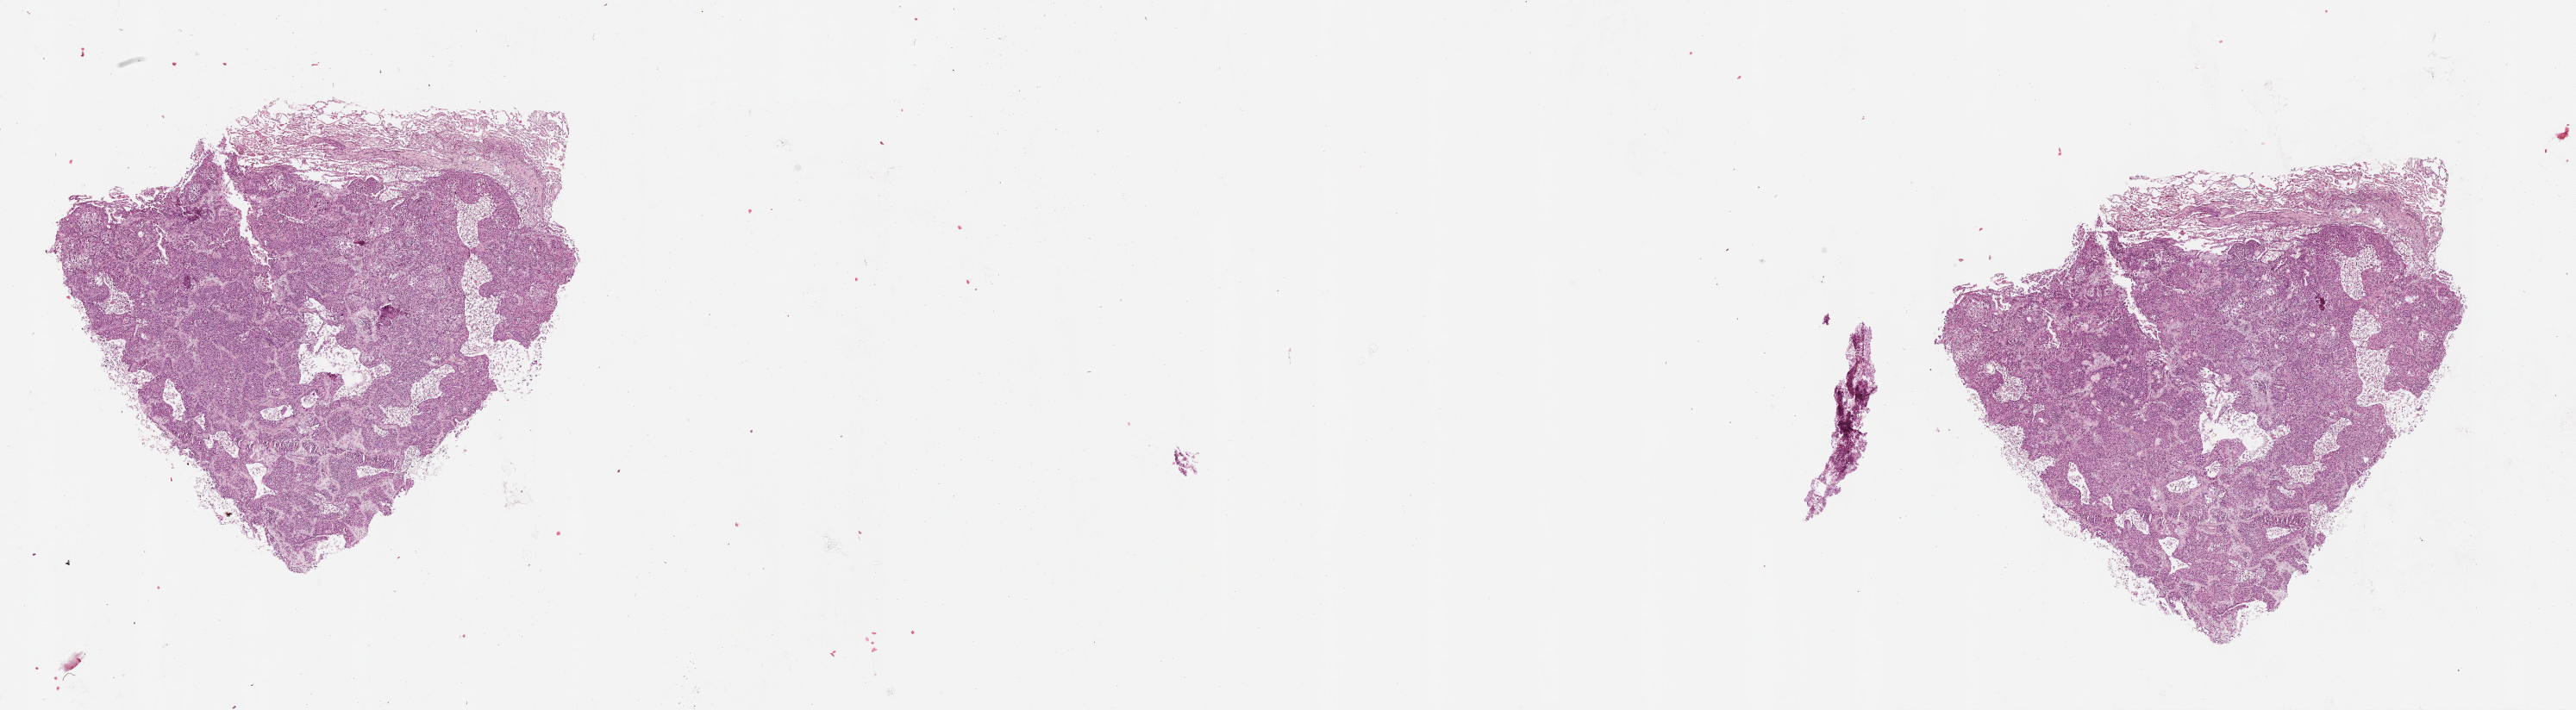
Whole-slide histology image, H&E-stained, a low-resolution overview of the entire scanned area, about 24.1 x 6.6 mm (from a 20x scan); tumour tissue sample, lung. 61-year-old male patient.
Patient diagnosis (cohort enrolment): squamous cell carcinoma (lung).